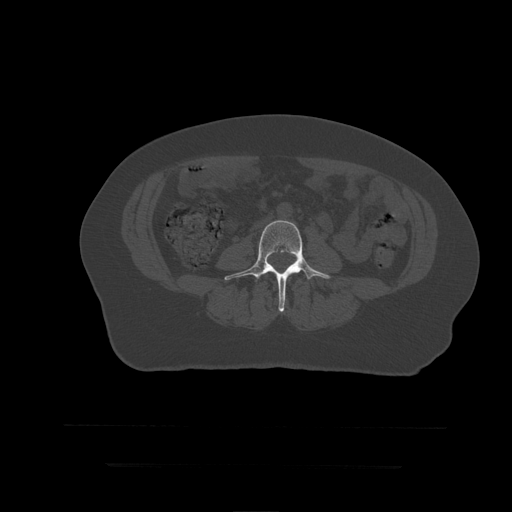
CT including the spine, one axial slice; slice 100 of 399 in the series (ordered by position); 120 kVp; bone window (W 1800 / L 400 HU); 1.25 mm slice thickness; 512 × 512 image matrix, field of view 450 × 450 mm. Patient age 41 years. From the clinical record (not read from this slice): primary cancer: breast.
Structures marked on this image (semi-automatically segmented with operator editing):
- L4 vertebra: bounding box (x1, y1, x2, y2) in pixels: (225, 220, 331, 313)